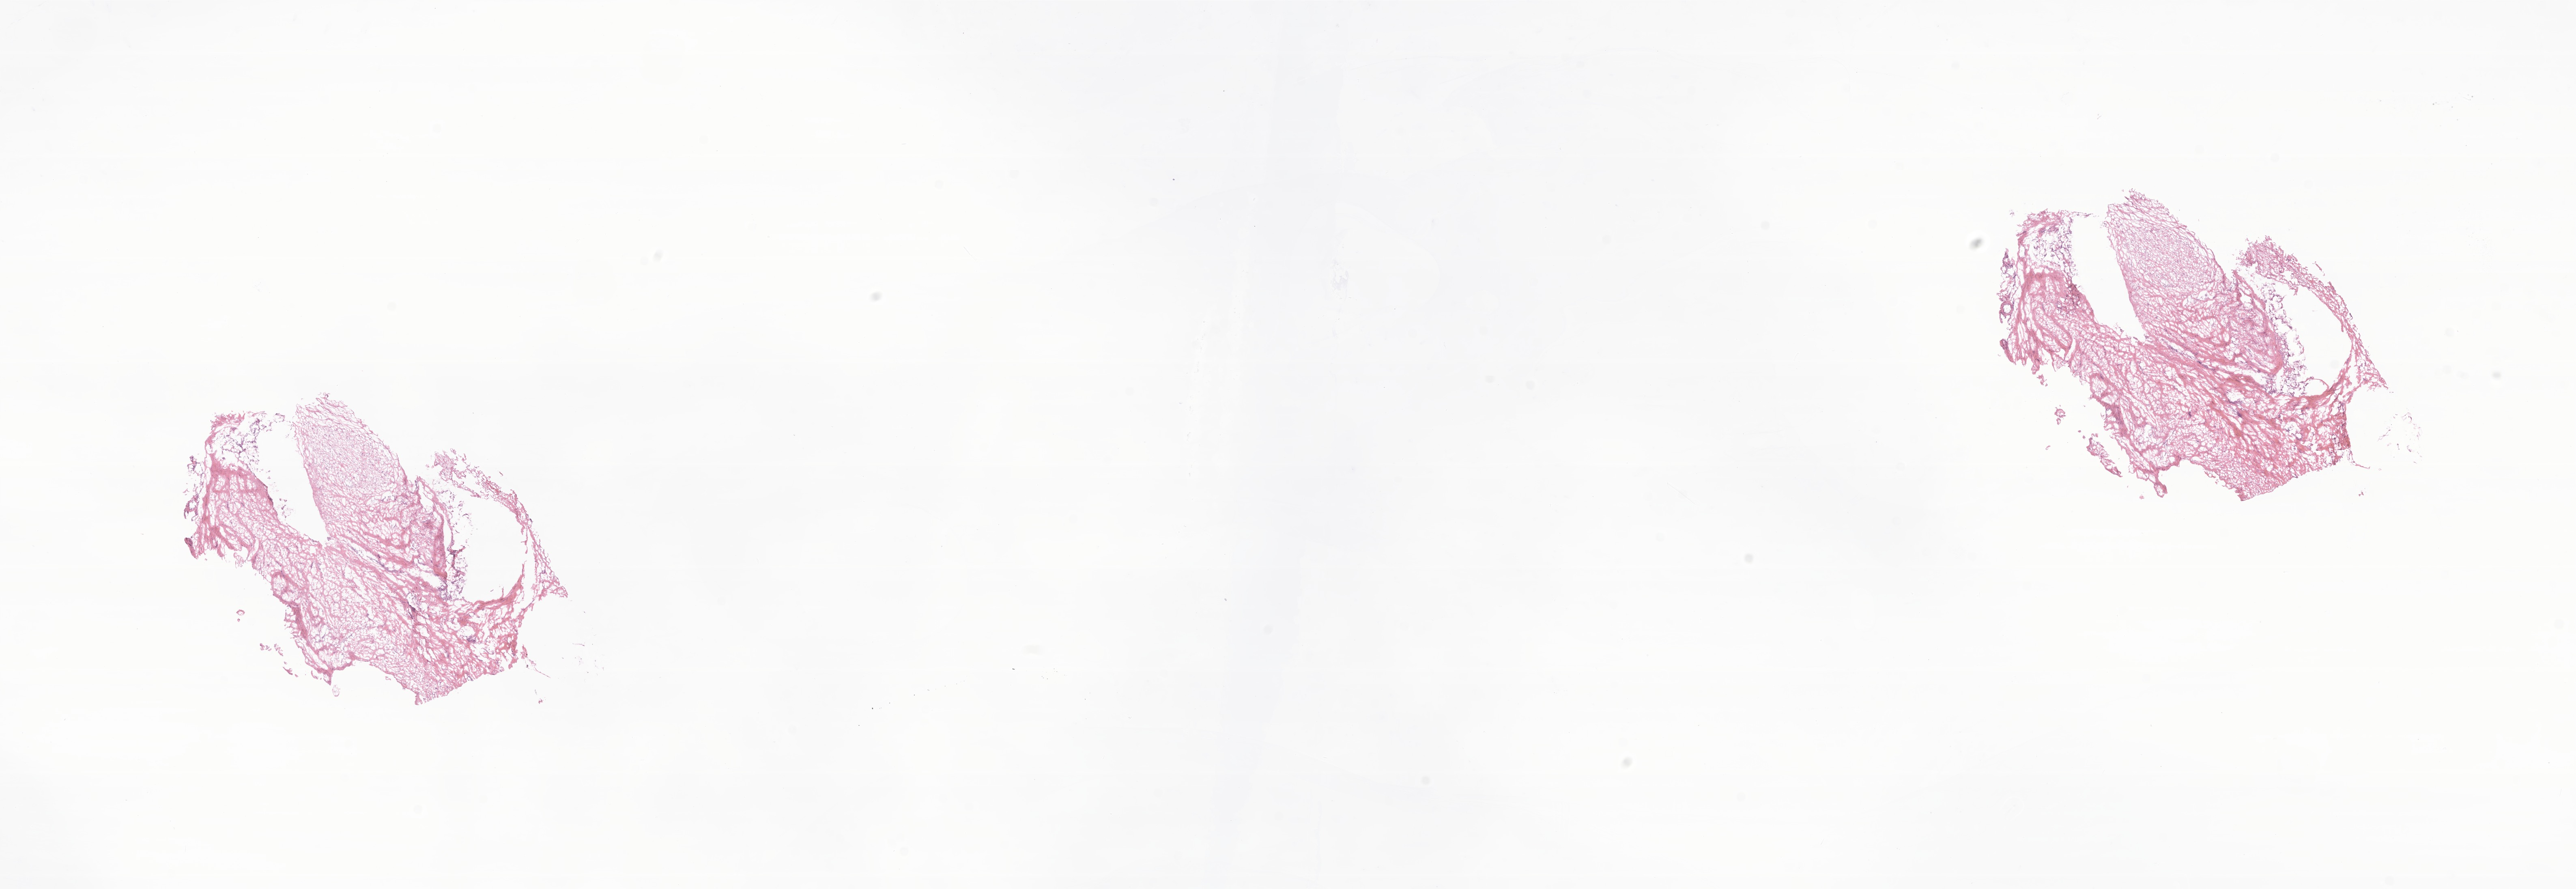
Haematoxylin and eosin whole-slide image of tumor tissue from the soft tissue of upper extremity — a low-resolution overview of the entire scanned area, about 26.8 x 9.2 mm. Frozen section (OCT-embedded). Male patient, age 502 days (about 1.4 years).
Recorded diagnosis: Myofibroblastic tumor, NOS.